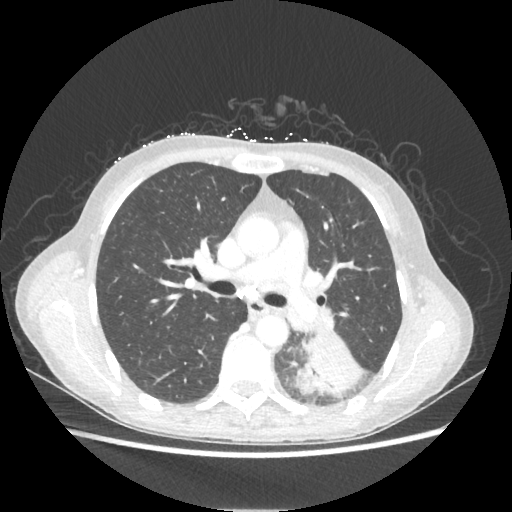
Chest CT, one axial slice. Slice 130 of 221 in the series (ordered by position). Reconstruction kernel STANDARD. Lung window (W 1500 / L -600 HU). 1.25 mm slice thickness. 512 × 512 image matrix. Female patient, age 53 years. Case-level facts recorded for this patient, not image findings: clinical TNM (as recorded): T3 N0 M0.
Annotated regions visible in this slice (rectangle marked by the reading radiologist):
- lung tumour (recorded histology: adenocarcinoma): box from (x=295, y=332) to (x=361, y=397) px